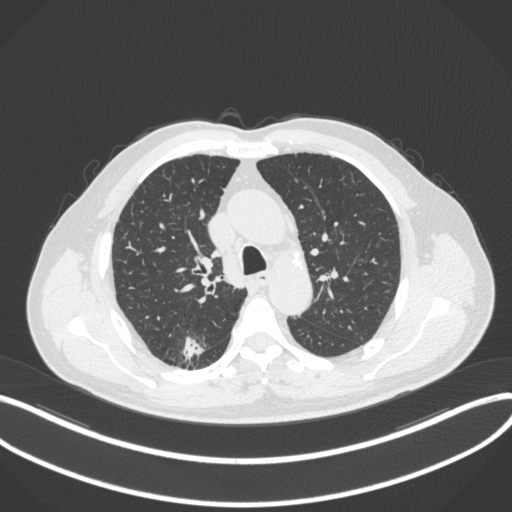
Chest CT, one axial slice; slice 260 of 366 in the series (ordered by position); lung window (W 1500 / L -600 HU); 1 mm slice thickness; 512 × 512 image matrix. Male patient, age 69 years. Case-level facts recorded for this patient, not image findings: clinical TNM (as recorded): T1b N0 M0; histopathological grade: G2-3.
Structures marked on this image (bounding box drawn by a radiologist):
- lung tumour (recorded histology: adenocarcinoma): bounding box <178,334,208,362> (left, top, right, bottom; pixels)